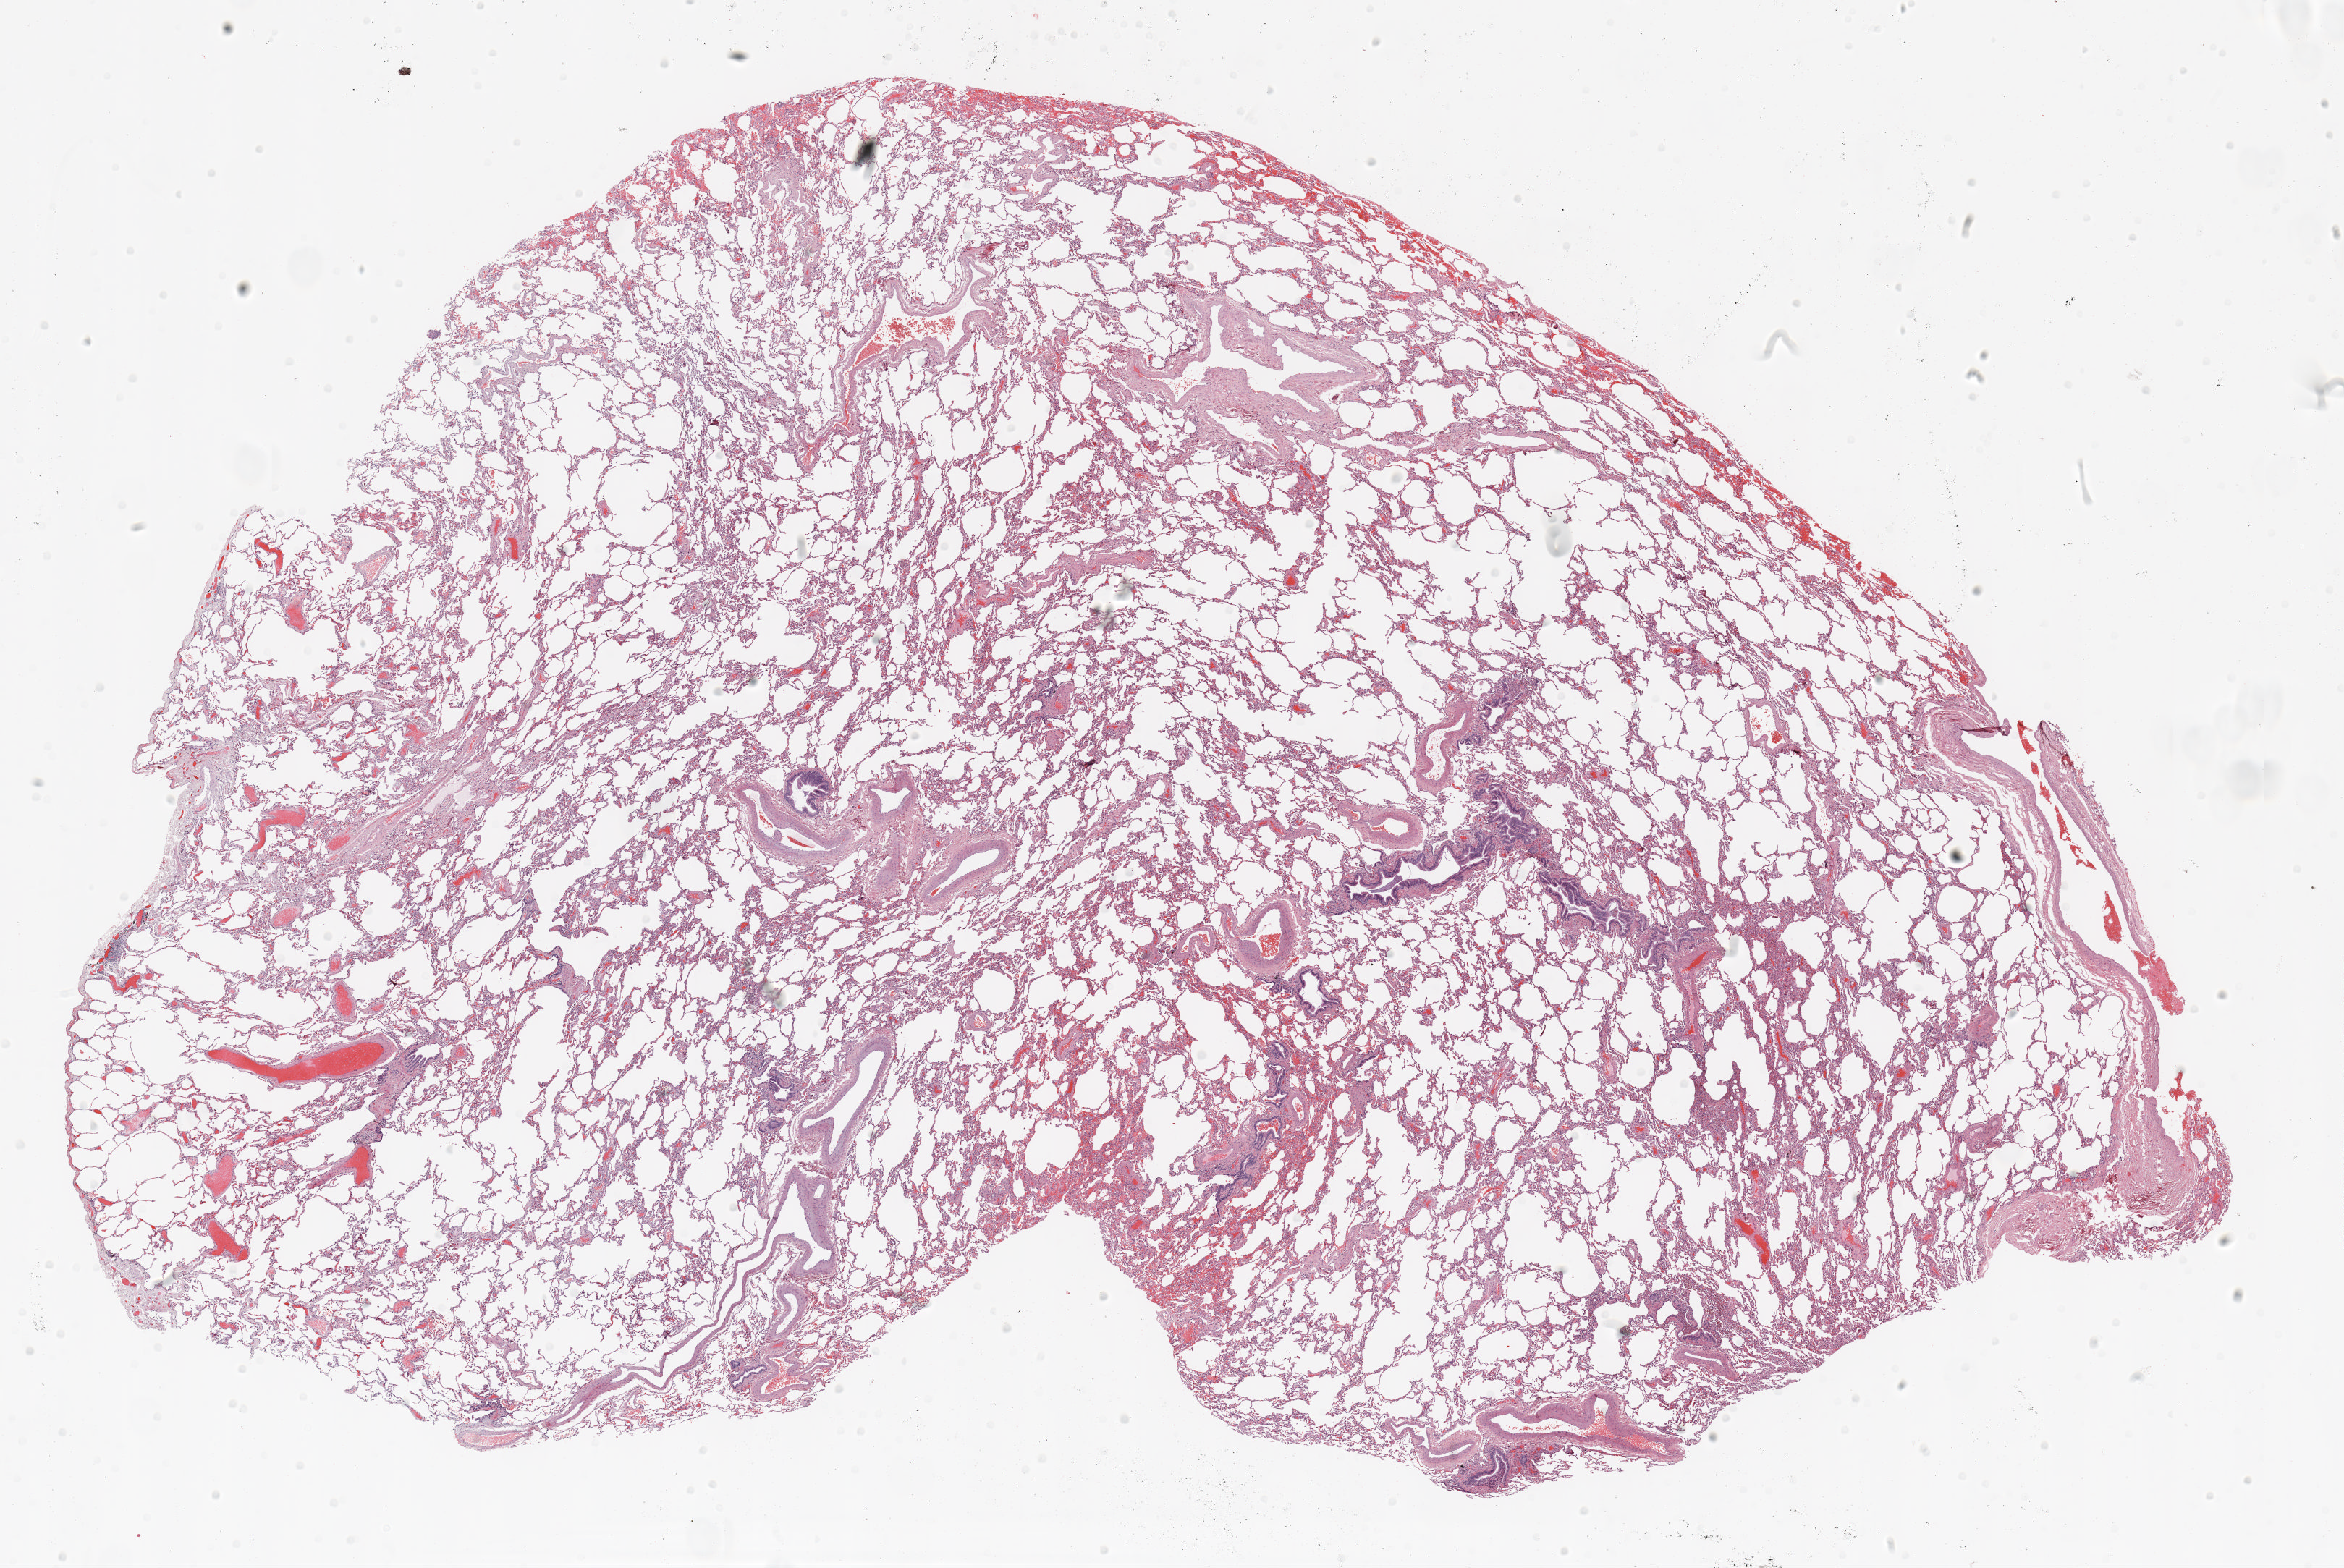
H&E-stained whole-slide image, low-resolution overview of the scanned area, about 26.0 x 17.4 mm (acquisition: 20x scan). FFPE section. Lung tissue. Male patient, aged 60 at enrolment. Grade: moderately differentiated (G2).
• primary tumour location (clinical record): right lower lobe
• participant's lung-cancer diagnosis: Squamous cell carcinoma, NOS (ICD-O-3 8070/3)
• stage (AJCC 6th edition): IB
• tumour size (pathology): 50 mm